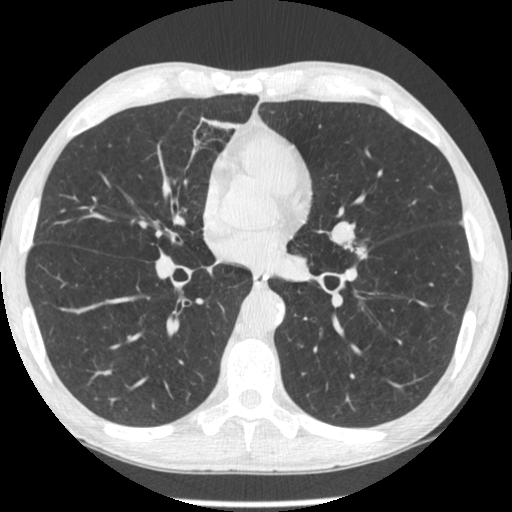
Low-dose screening chest CT, one axial slice. Slice 134 of 293 in the series (ordered by position). Reconstruction kernel STANDARD. Lung window (W 1500 / L -600 HU). 1.25 mm slice thickness. 512 × 512 image matrix, field of view 326 × 326 mm.
Outlined on this slice (manually delineated by an expert):
- lesion 1 (tumor, upper lobe of left lung): box from (x=353, y=247) to (x=366, y=255) px